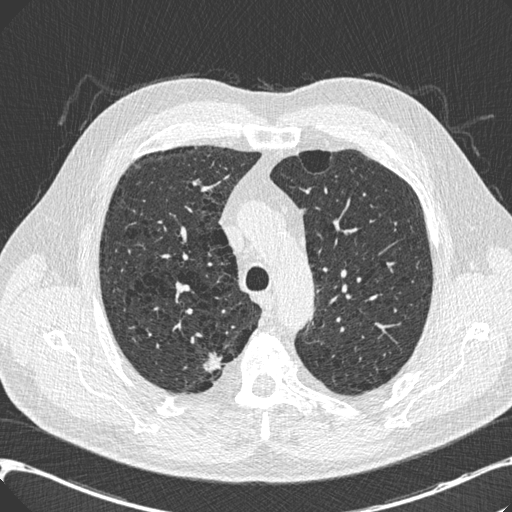
Low-dose screening chest CT, one axial slice; slice 148 of 197 in the series (ordered by position); lung window (W 1500 / L -600 HU); 0.75 mm slice thickness; 512 × 512 image matrix, field of view 367 × 367 mm.
Annotated regions visible in this slice (manually delineated by an expert):
- lesion 1 (tumor, upper lobe of right lung): bounding box <203,350,222,372> (left, top, right, bottom; pixels)